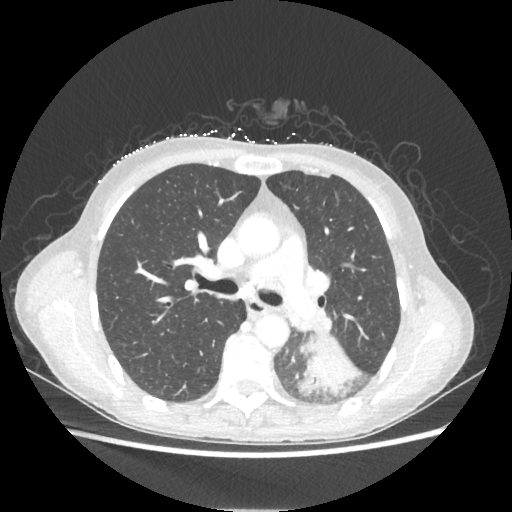
Chest CT, one axial slice; position 132 of 221 along the scan axis; 80 kVp; lung window (W 1500 / L -600 HU); 1.25 mm slice thickness; 512 × 512 image matrix, field of view 360 × 360 mm. Female patient, age 53 years. From the clinical record (not read from this slice): clinical TNM (as recorded): T3 N0 M0.
Outlined on this slice (rectangle marked by the reading radiologist):
- lung tumour (recorded histology: adenocarcinoma): bounding box (x1, y1, x2, y2) in pixels: (298, 336, 361, 396)